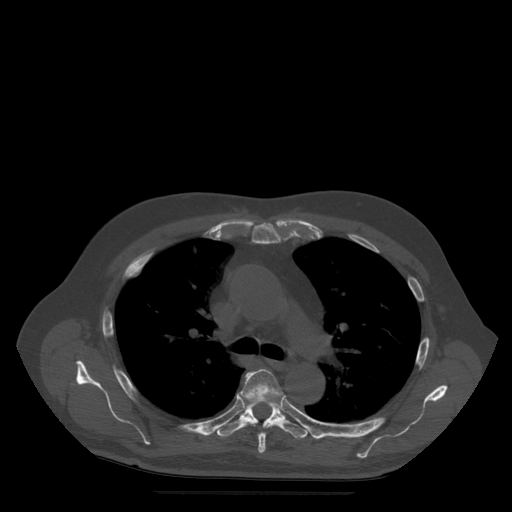
CT including the spine, one axial slice; position 363 of 522 along the scan axis; bone window (W 1800 / L 400 HU); 512 × 512 image matrix, field of view 420 × 420 mm. Patient age 72 years. From the clinical record (not read from this slice): primary cancer: prostate.
Structures marked on this image (semi-automatic segmentation, software-assisted and operator-edited):
- T5 vertebra: bounding box (x1, y1, x2, y2) in pixels: (241, 369, 283, 454)
- T6 vertebra: (217, 400, 308, 439)